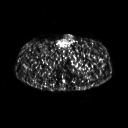
FDG PET of an extremity soft-tissue mass (from a PET/CT study), one axial slice. Position 265 of 267 along the scan axis. 3.27 mm slice thickness. 128 × 128 image matrix, field of view 500 × 500 mm. Patient: male, 27 years. Case-level facts recorded for this patient, not image findings: histological type: extraskeletal osteosarcoma; grade: high; site of the primary tumour: left adductur.
Structures marked on this image (expert contour drawn on MRI and transferred to this co-registered scan by the dataset authors):
- gross tumour volume (mass): bounding box (x1, y1, x2, y2) in pixels: (70, 49, 97, 74)